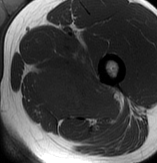
MRI of an extremity soft-tissue mass, one axial slice; position 57 of 70 along the scan axis; MR volume resampled by the dataset authors to the PET/CT grid (not the native acquisition matrix); 3.27 mm slice thickness; 157 × 163 image matrix, field of view 153 × 159 mm. Male patient. From the clinical record (not read from this slice): histological type: extraskeletal osteosarcoma; grade: high; site of the primary tumour: left adductur.
Annotated regions visible in this slice (expert contour drawn on MRI and transferred to this co-registered scan by the dataset authors):
- gross tumour volume (mass): box from (x=31, y=46) to (x=121, y=121) px